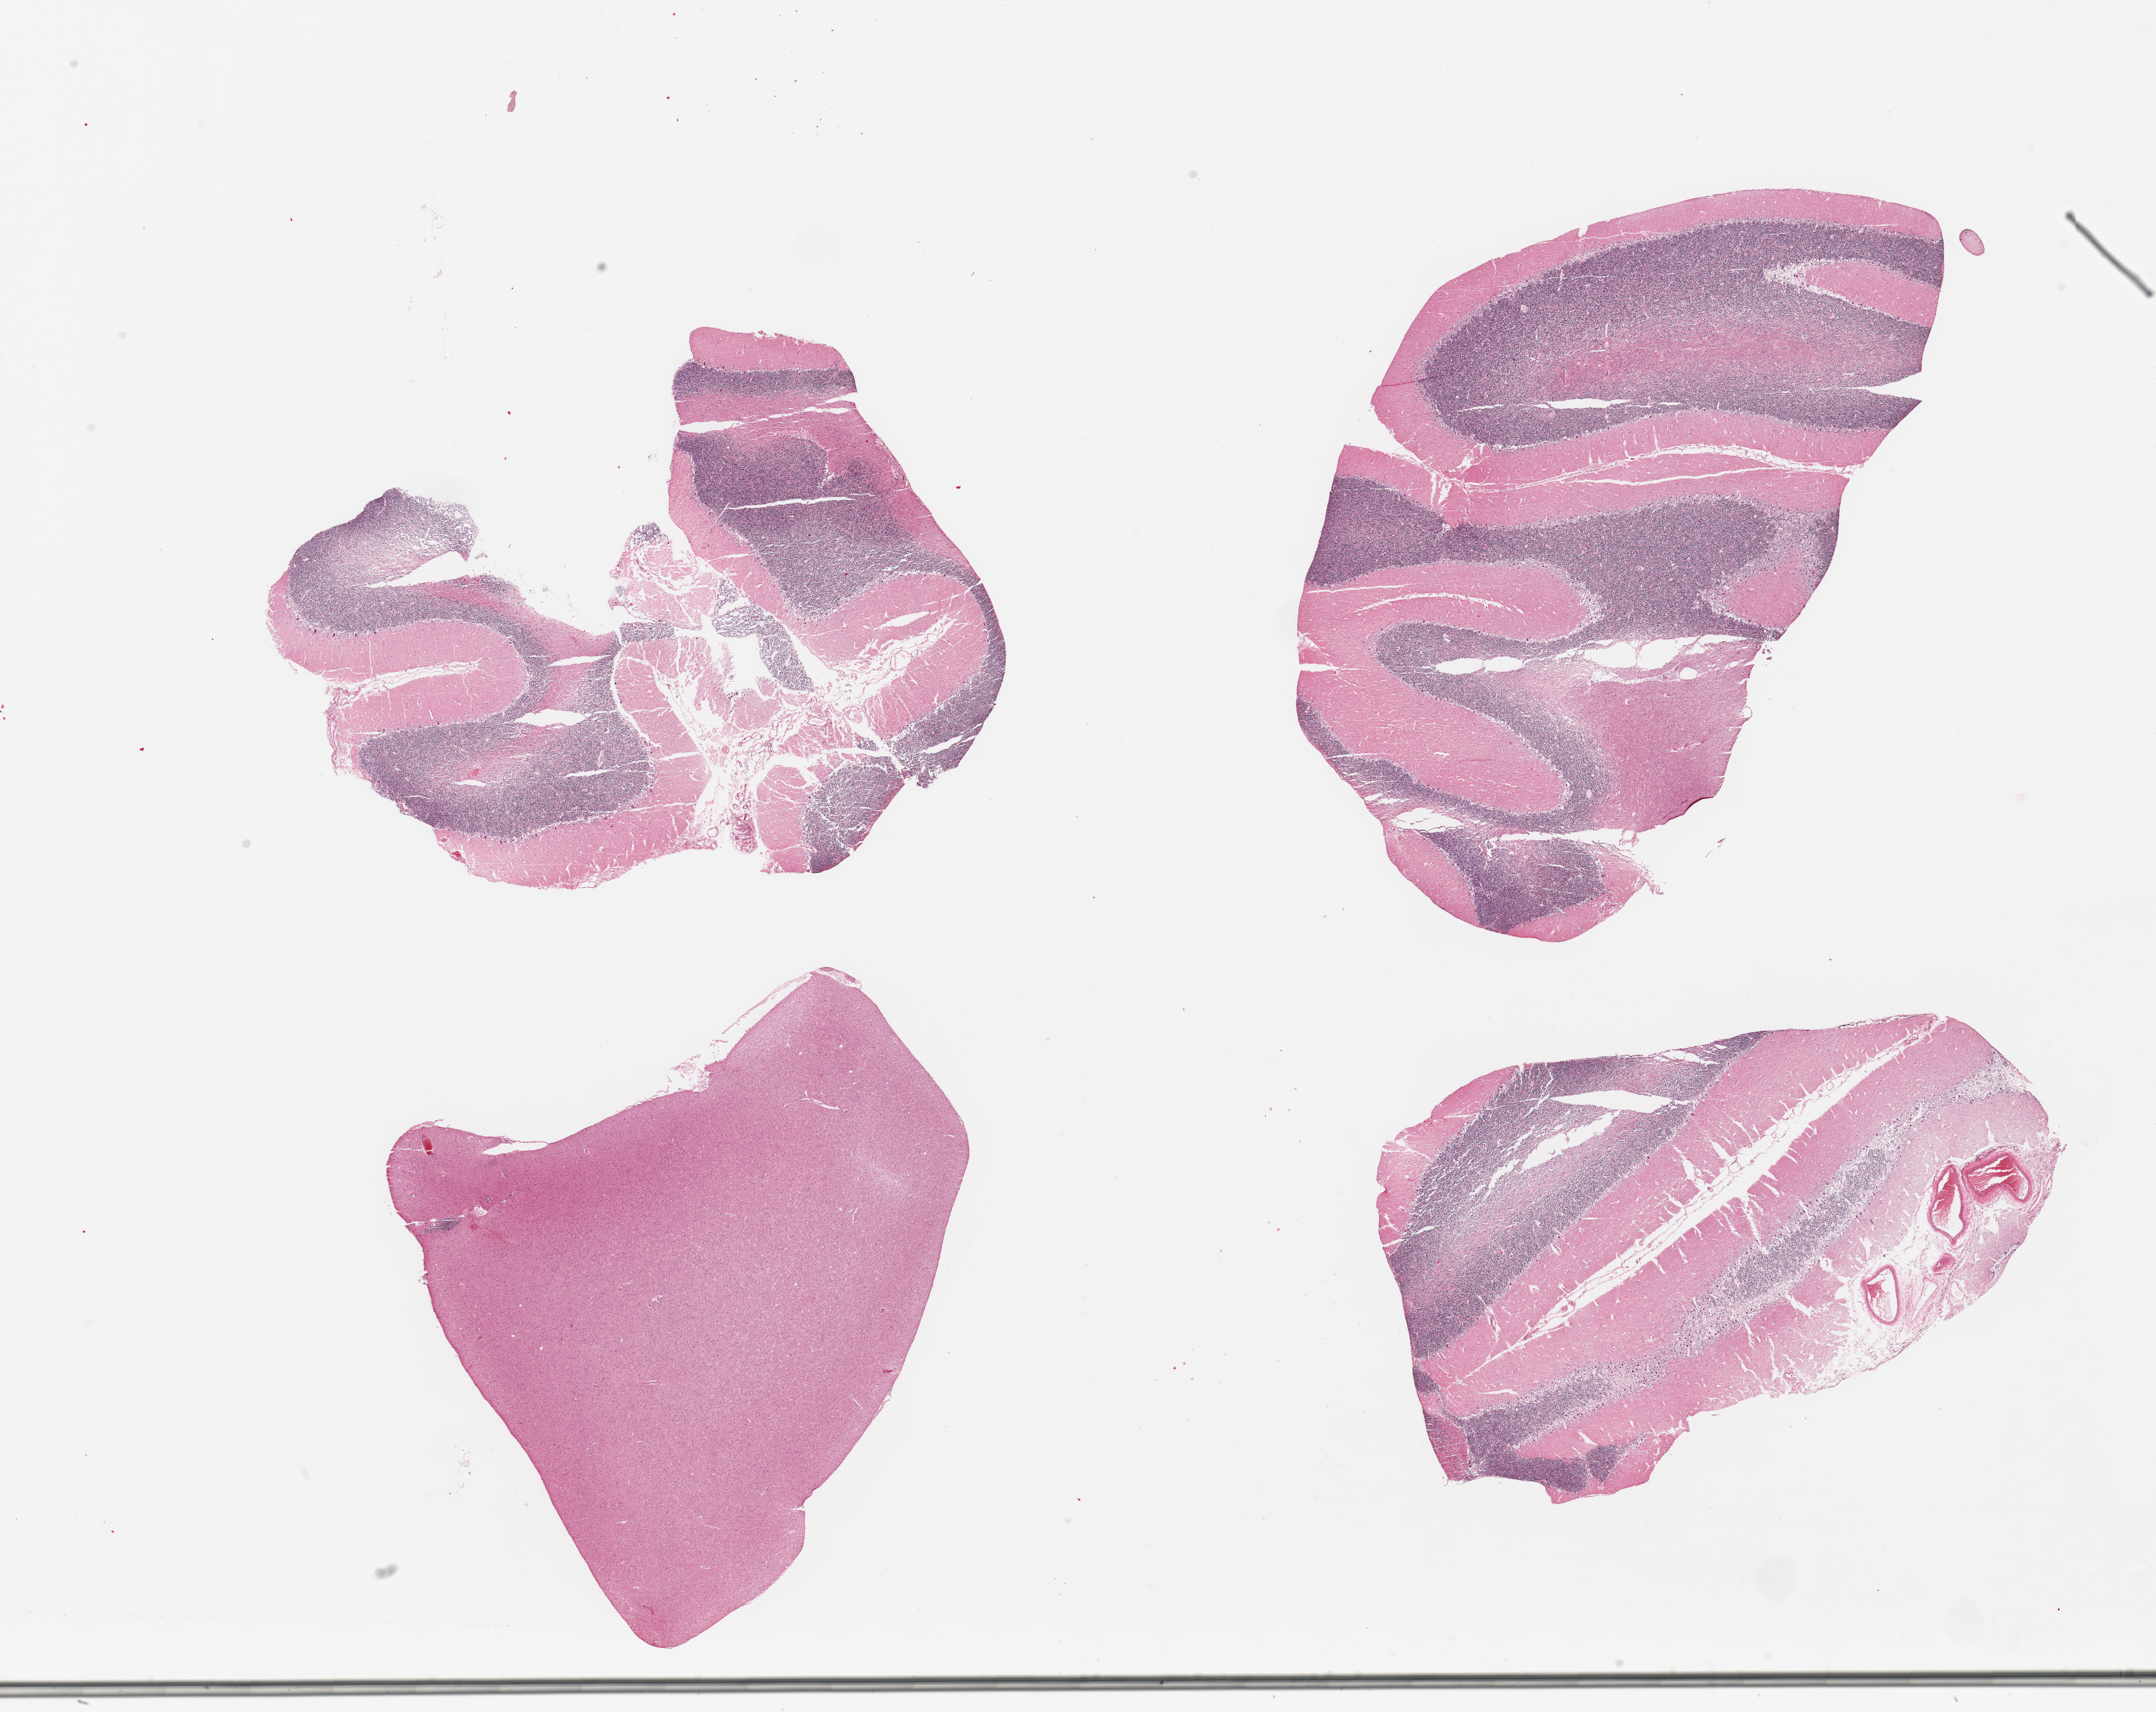
Haematoxylin and eosin whole-slide image, whole scanned area (about 25.6 x 20.3 mm) shown as a low-resolution overview; PAXgene-fixed, paraffin-embedded tissue; target tissue: cerebellum; tissue donor sample. Donor: male.
* pathologist's review note for this sample: 3 pieces, no abnormalities; one extraneous section of cortex; sample with caution